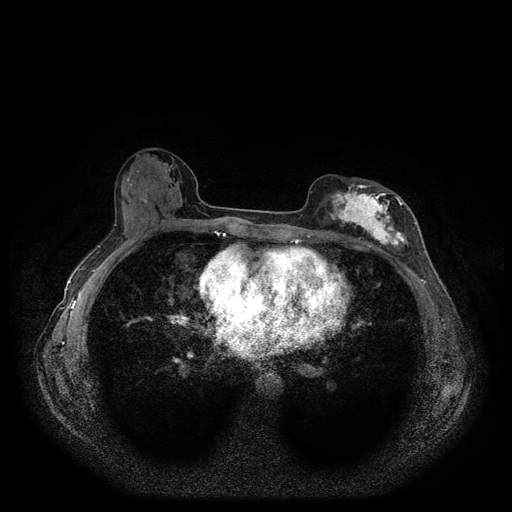
Breast MRI (dynamic contrast-enhanced, multi-phase), one axial slice; slice 52 of 116 in the series (ordered by position); dynamic contrast-enhanced series, time point 2 of 5 at this slice position (early post-contrast); 1.5 T; TE 2.6 ms, TR 5.3 ms; 2 mm slice thickness; 512 × 512 image matrix. Patient: female, 51 years.
Outlined on this slice (semi-automatic segmentation, software-assisted and operator-edited):
- breast lesion (labelled 'tumour' in the annotation; benign lesions carry a separate 'benign' label): bounding box <325,182,414,253> (left, top, right, bottom; pixels)